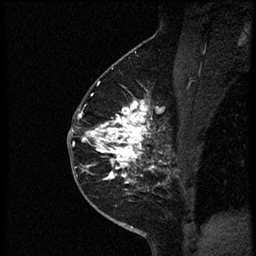
Breast MRI (dynamic contrast-enhanced), one sagittal slice; position 35 of 56 along the scan axis; dynamic contrast-enhanced study with each time point stored as its own series, time point 2 of 4 at this slice position (early post-contrast, ordered by acquisition time); 1.5 T; TE 4.2 ms, TR 18.9 ms; 2 mm slice thickness; 256 × 256 image matrix, field of view 200 × 200 mm. Female patient. From the clinical record (not read from this slice): setting: breast cancer imaged before/during neoadjuvant chemotherapy; receptor status: HER2-positive.
Outlined on this slice (semi-automatically segmented with operator editing):
- analysis volume of interest (the breast-tissue region the enhancement analysis was run in; not a lesion): bounding box (x1, y1, x2, y2) in pixels: (78, 85, 174, 189)
- tumour enhancement mask (voxels above the 100 % enhancement threshold inside the analysis volume of interest): (84, 96, 169, 188)